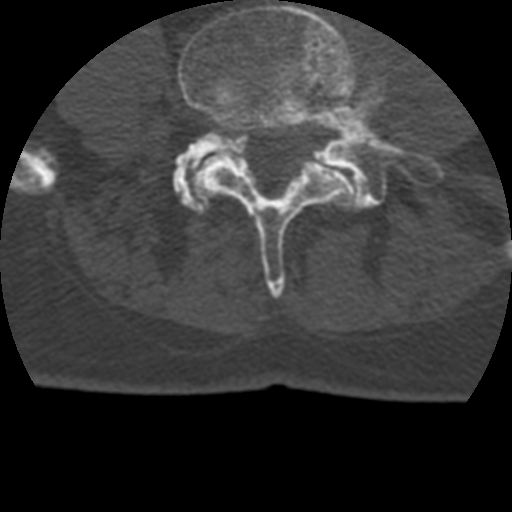
CT including the spine, one axial slice; slice 57 of 399 in the series (ordered by position); reconstruction kernel STANDARD; 120 kVp; bone window (W 1800 / L 400 HU); 1.25 mm slice thickness; 512 × 512 image matrix, field of view 160 × 160 mm. Patient age 69 years. Case-level facts recorded for this patient, not image findings: primary cancer: prostate.
Structures marked on this image (semi-automatically segmented with operator editing):
- L4 vertebra: box from (x=178, y=0) to (x=358, y=298) px
- L5 vertebra: (x=173, y=77)–(x=432, y=210)